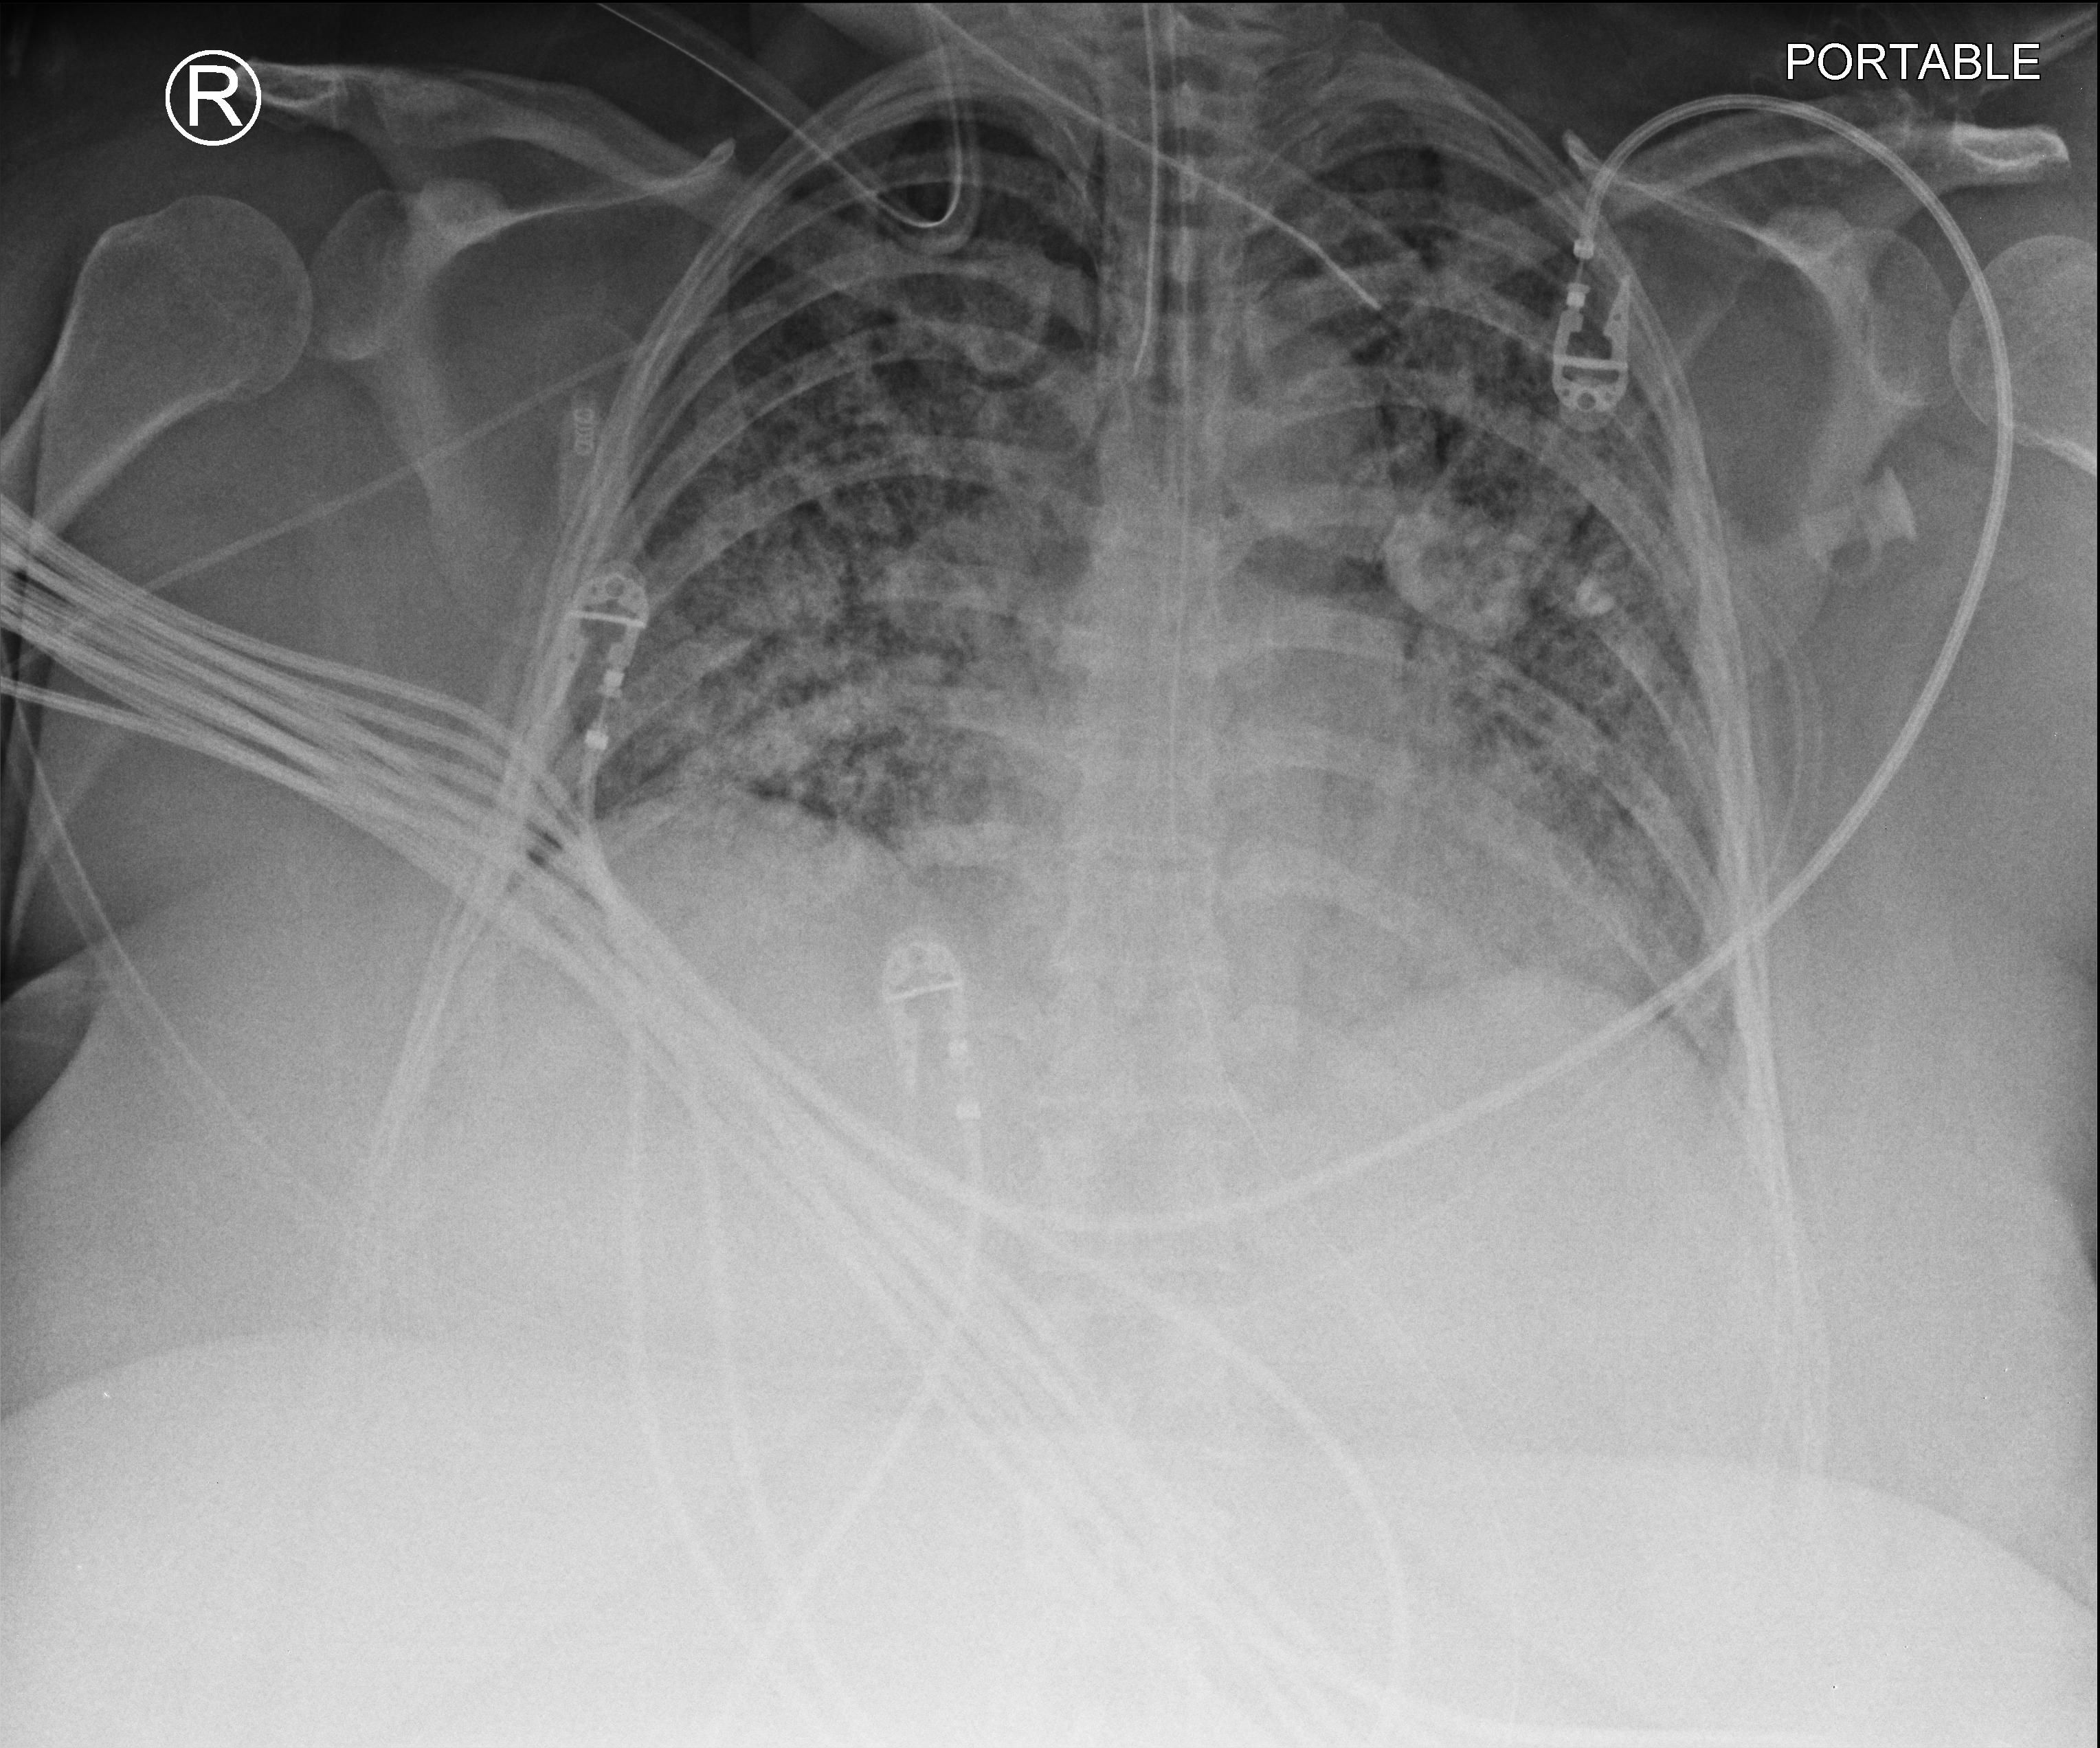
Portable chest radiograph; anteroposterior (AP) projection. Patient hospitalised with COVID-19; female, aged 18–59 years.
Admission-level facts for this patient (not findings on this image; timing relative to this image not recorded): mechanically ventilated during this hospital stay: yes.